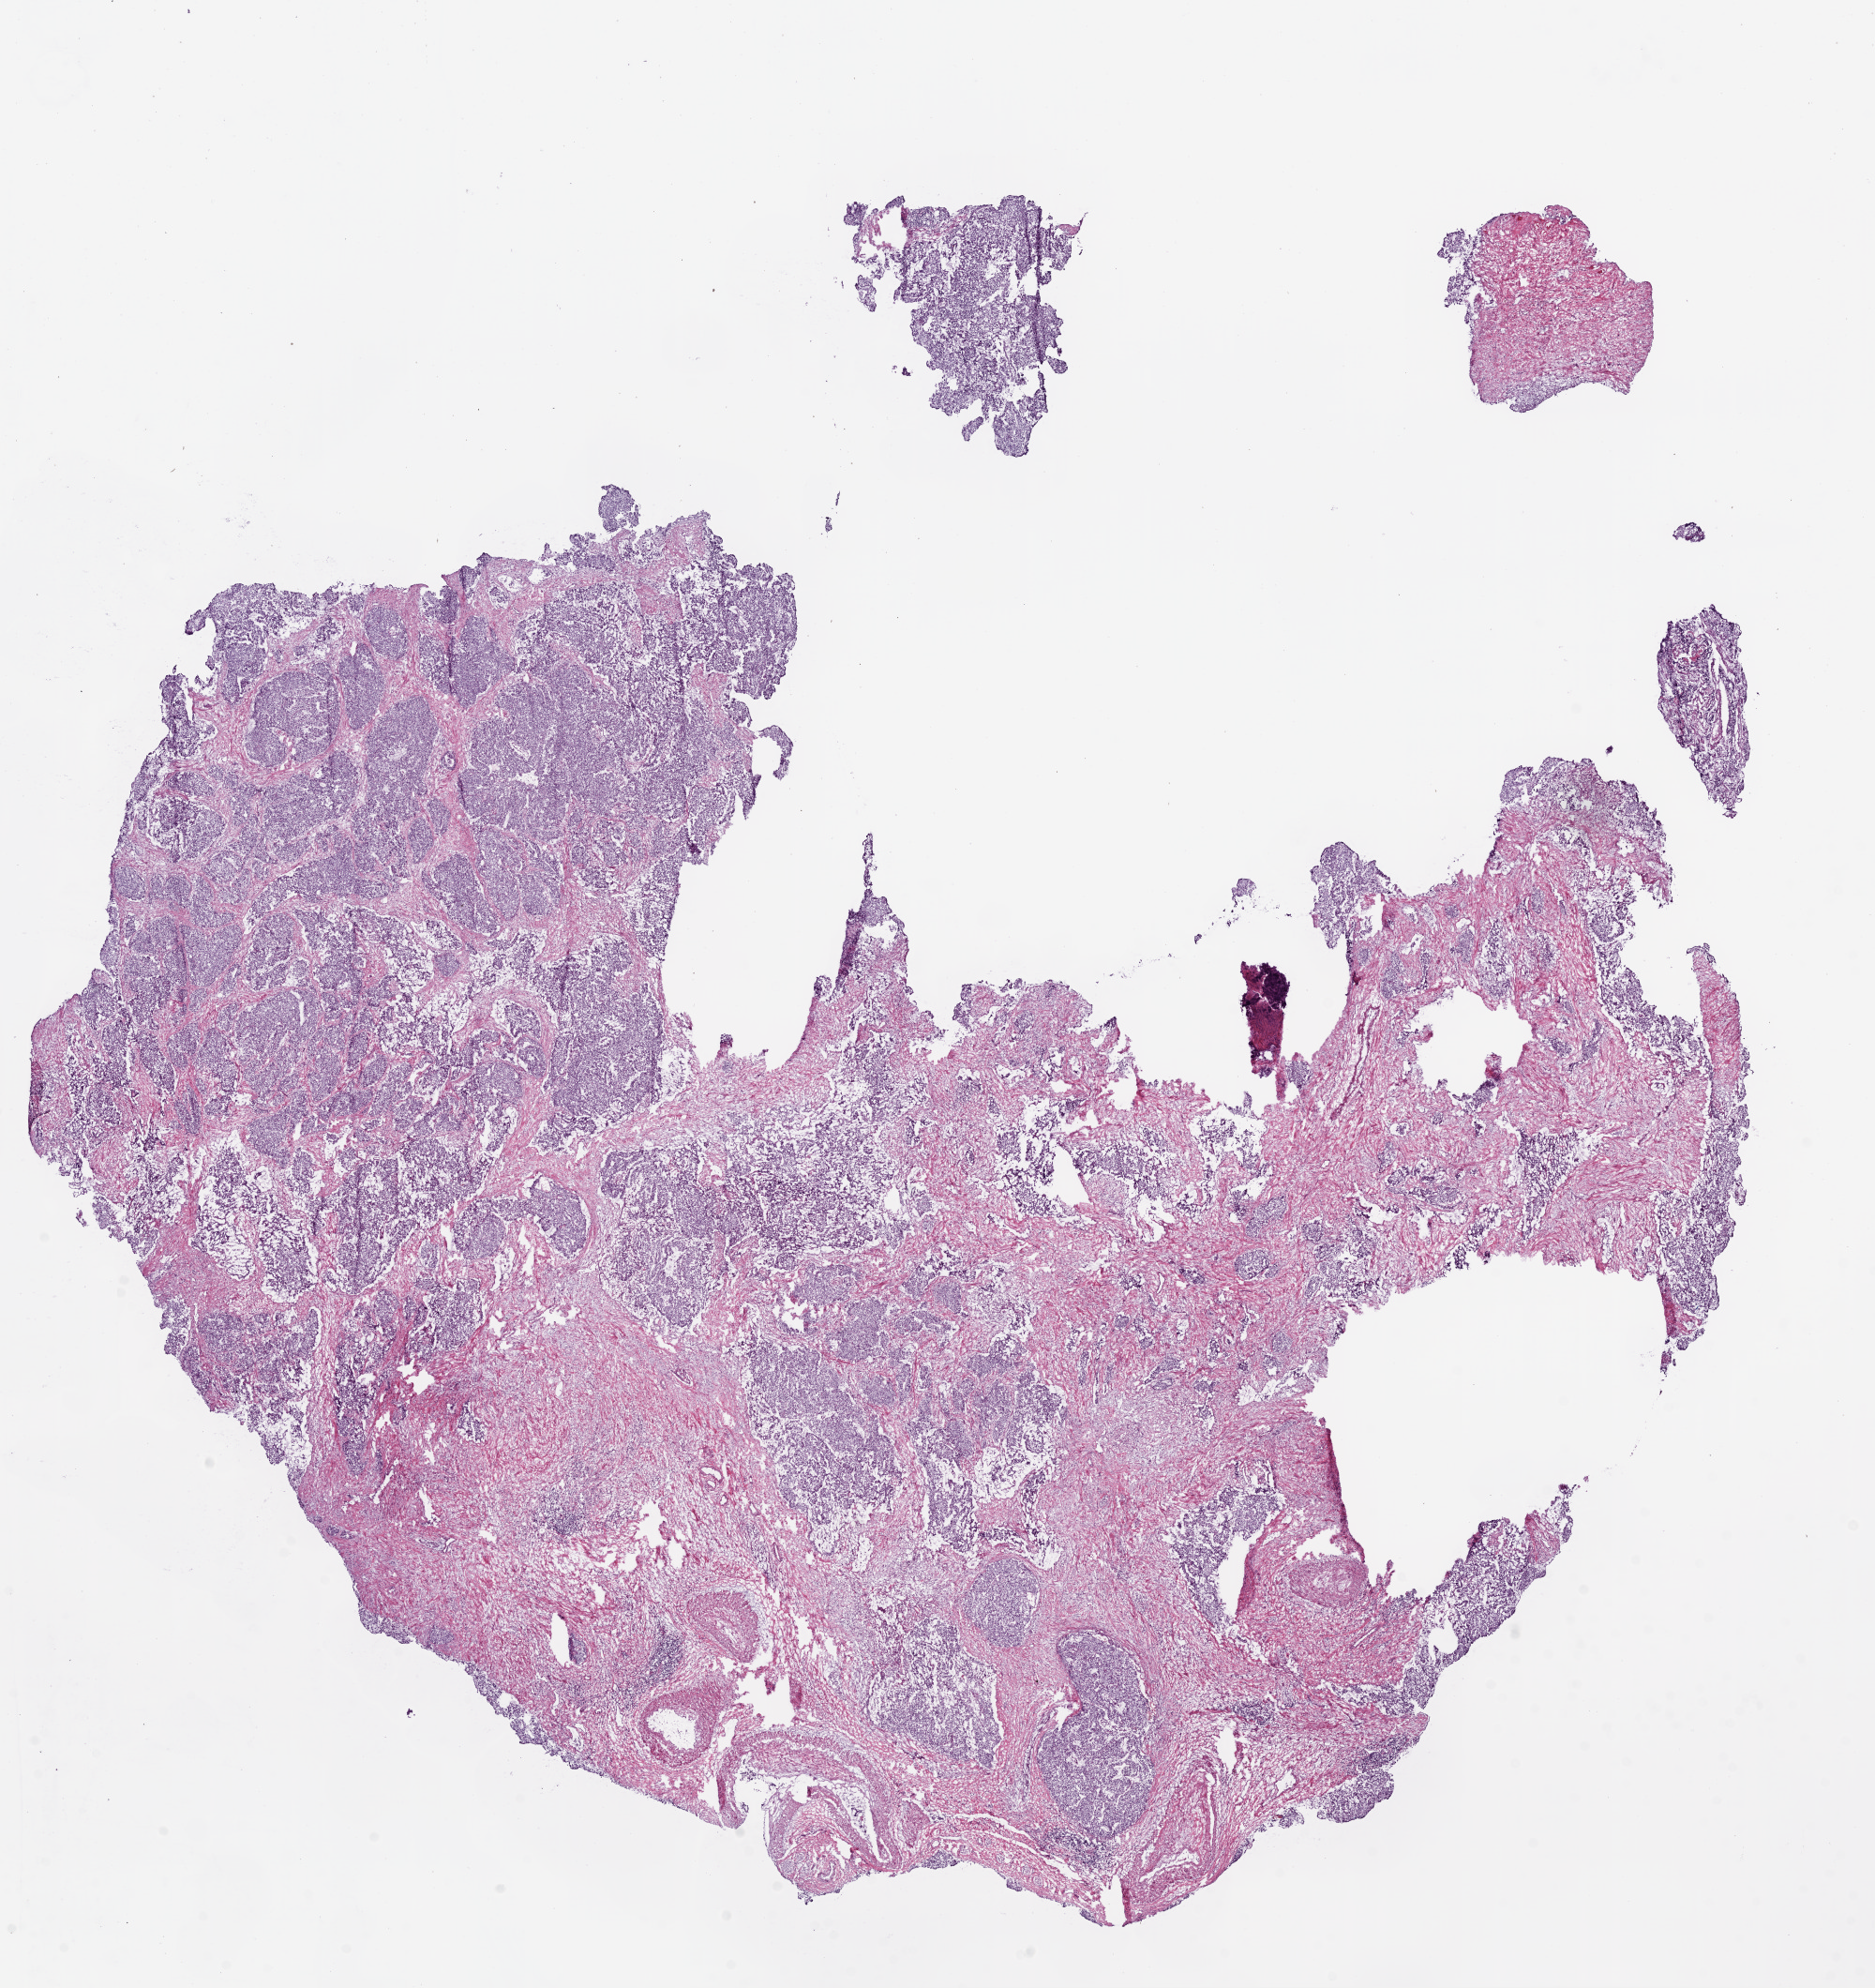
Whole-slide histology image, H&E-stained, whole scanned area (about 16.0 x 17.0 mm, from a 20x scan) shown as a low-resolution overview; frozen section from the bottom of the tissue portion; sample: primary tumour, prostate. Male patient; age at initial diagnosis 67 years. Gleason score: 9 (4+5). Slide review estimates, as recorded: tumour cells 50%, tumour nuclei 55%, normal cells 10%, stromal cells 35%, necrosis 5%. Inflammatory infiltration, as recorded: lymphocyte infiltration 5%, monocyte infiltration 5%, neutrophil infiltration 0%.
- lymph nodes positive (case pathology): 0 of 8 examined
- laterality: bilateral
- pathologic diagnosis: Acinar cell carcinoma